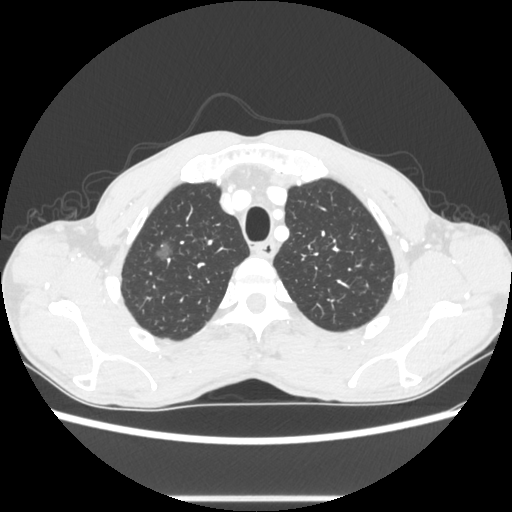
Chest CT, one axial slice. Position 237 of 289 along the scan axis. 100 kVp. Lung window (W 1500 / L -600 HU). 1.25 mm slice thickness. 512 × 512 image matrix, field of view 350 × 350 mm. Patient: male, 54 years. From the clinical record (not read from this slice): clinical TNM (as recorded): T1a N0 M0.
Outlined on this slice (rectangle marked by the reading radiologist):
- lung tumour (recorded histology: adenocarcinoma): bounding box [x1, y1, x2, y2] px = [150, 231, 179, 267]